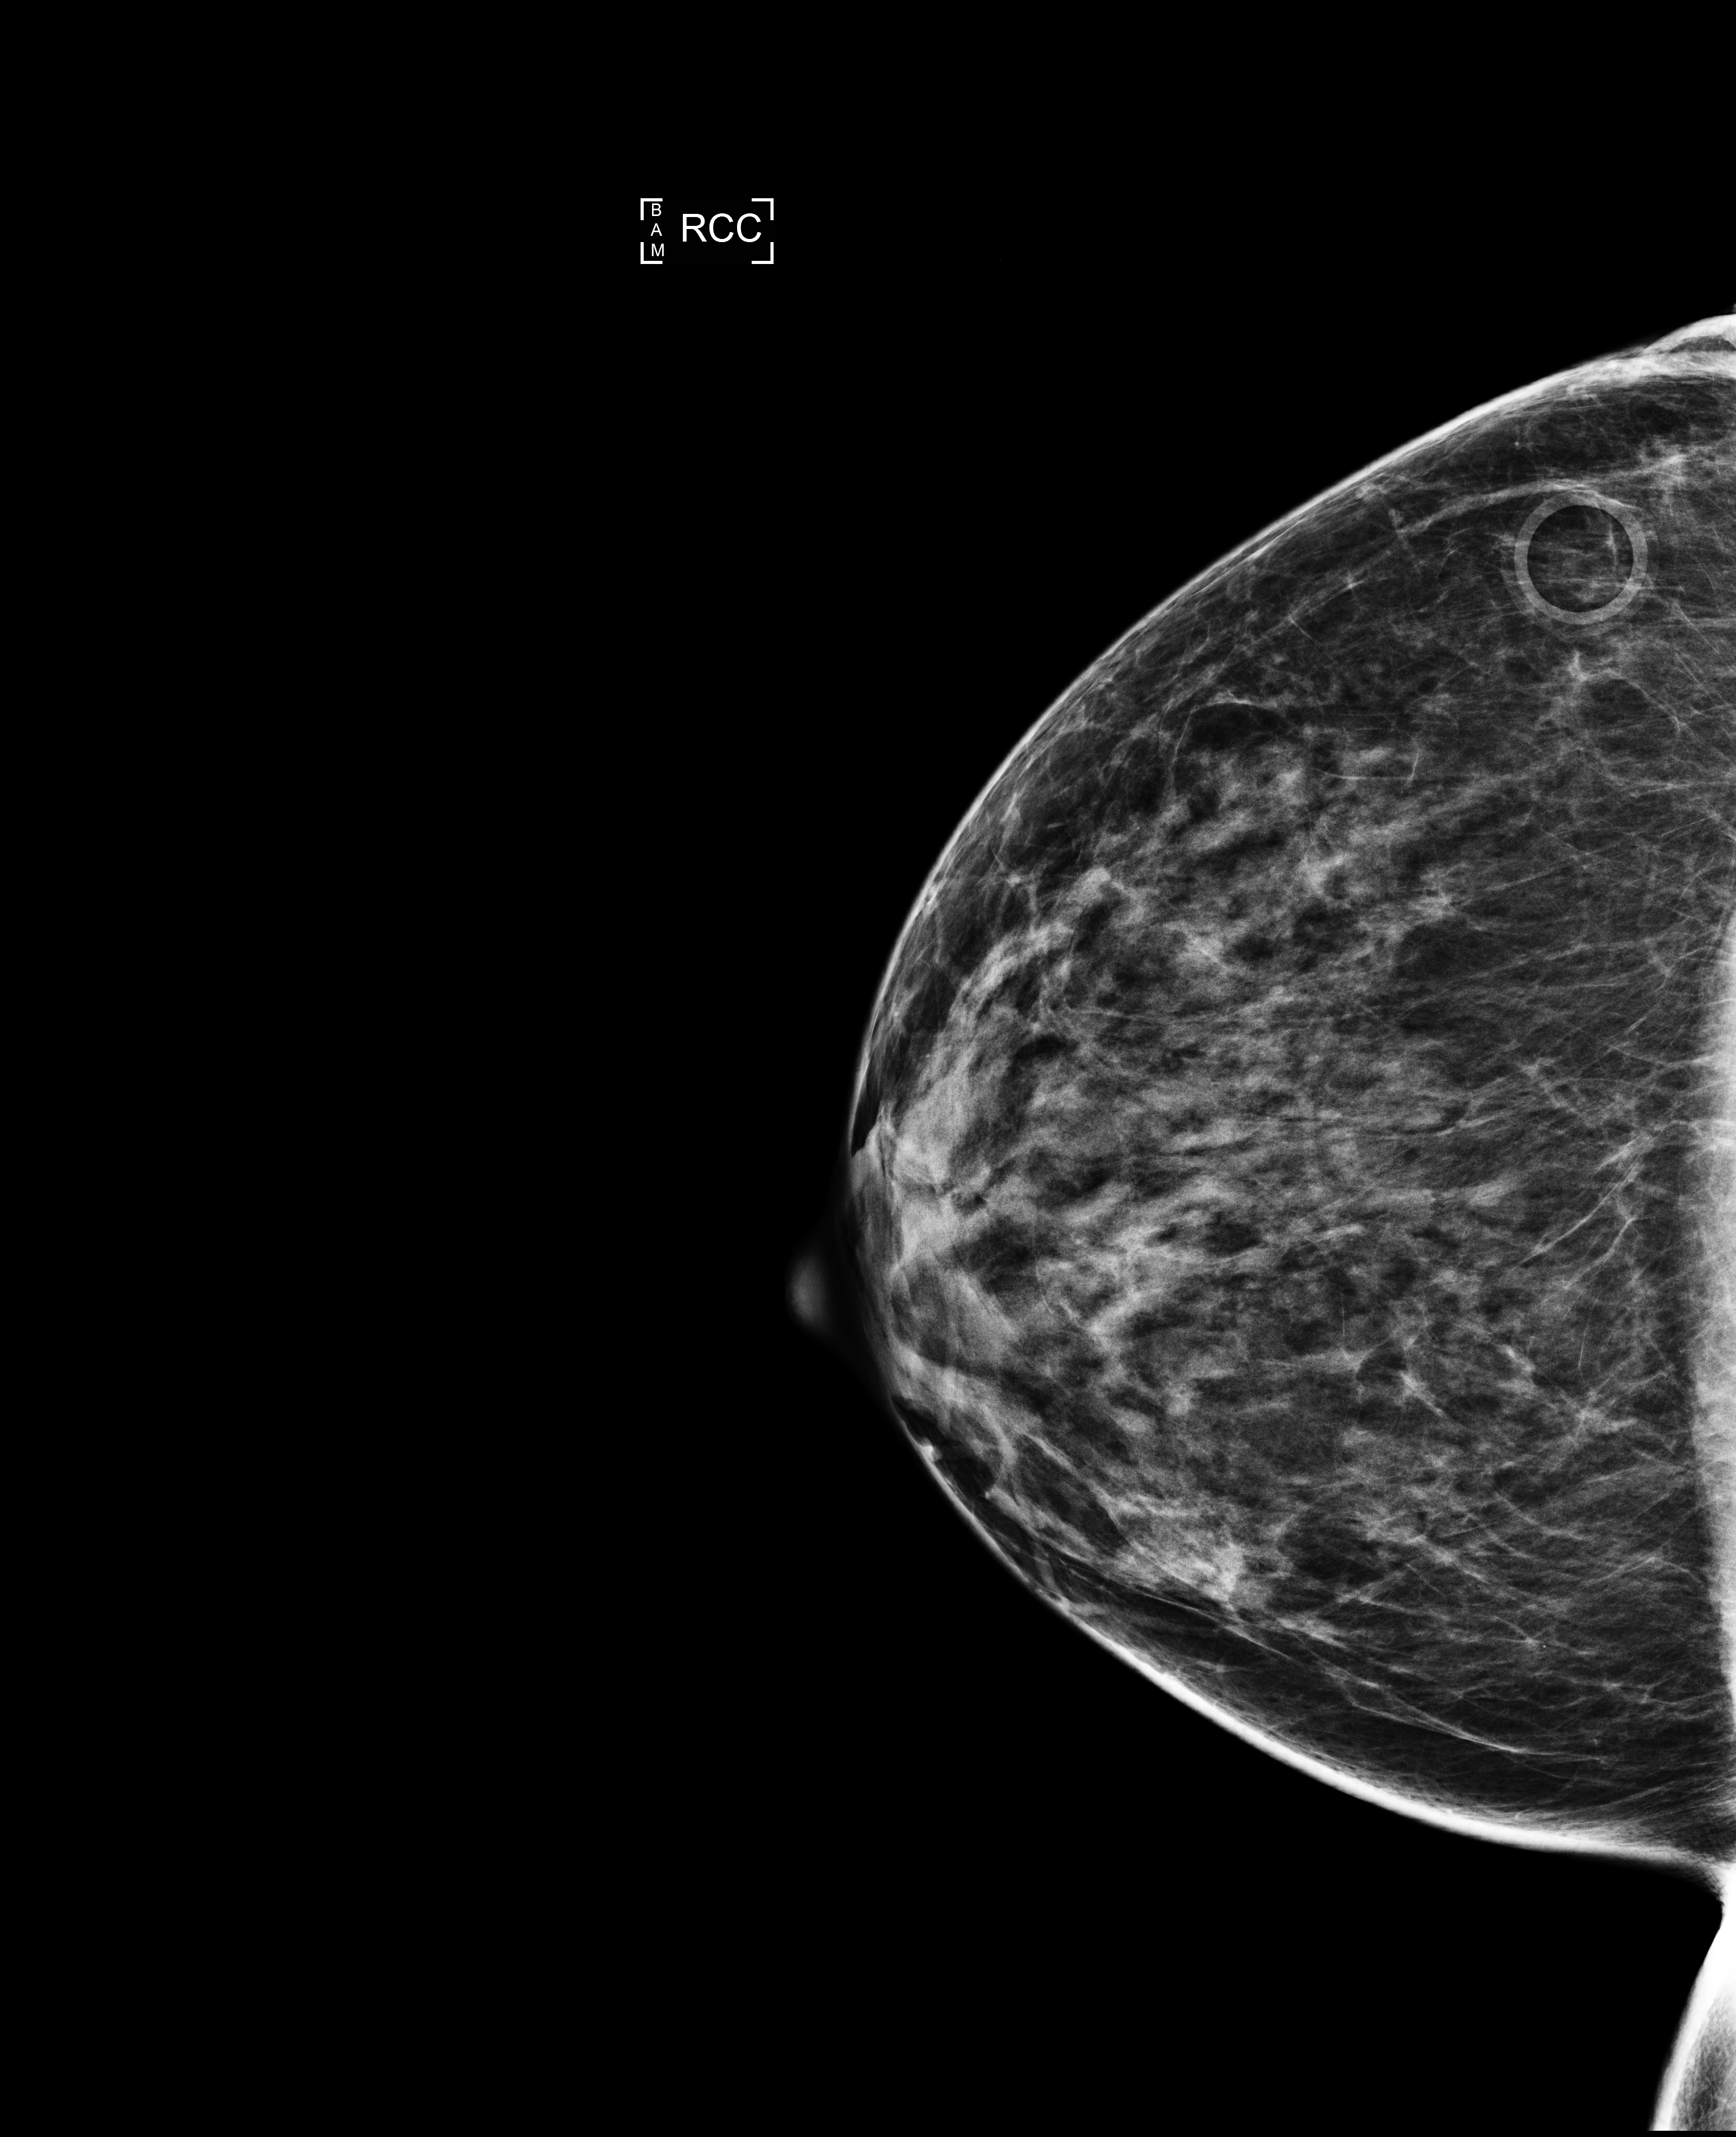
Annual screening mammography examination. Female patient, age 44 years.
Image type: full-field digital mammogram. Breast: right. Projection: CC view.